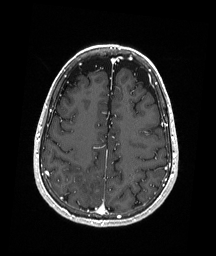
Brain MRI from a brain-tumour surgery series, one axial slice. Slice 70 of 192 in the series (ordered by position). T1-weighted post-contrast. 1 mm slice thickness. 216 × 256 image matrix, field of view 211 × 250 mm. From the clinical record (not read from this slice): histopathology: Astrocytoma; WHO grade: 3; IDH mutation: yes; tumour location: Right Parietal.
Annotated regions visible in this slice (manually delineated by an expert):
- tumour: bounding box [x1, y1, x2, y2] px = [95, 189, 100, 192]